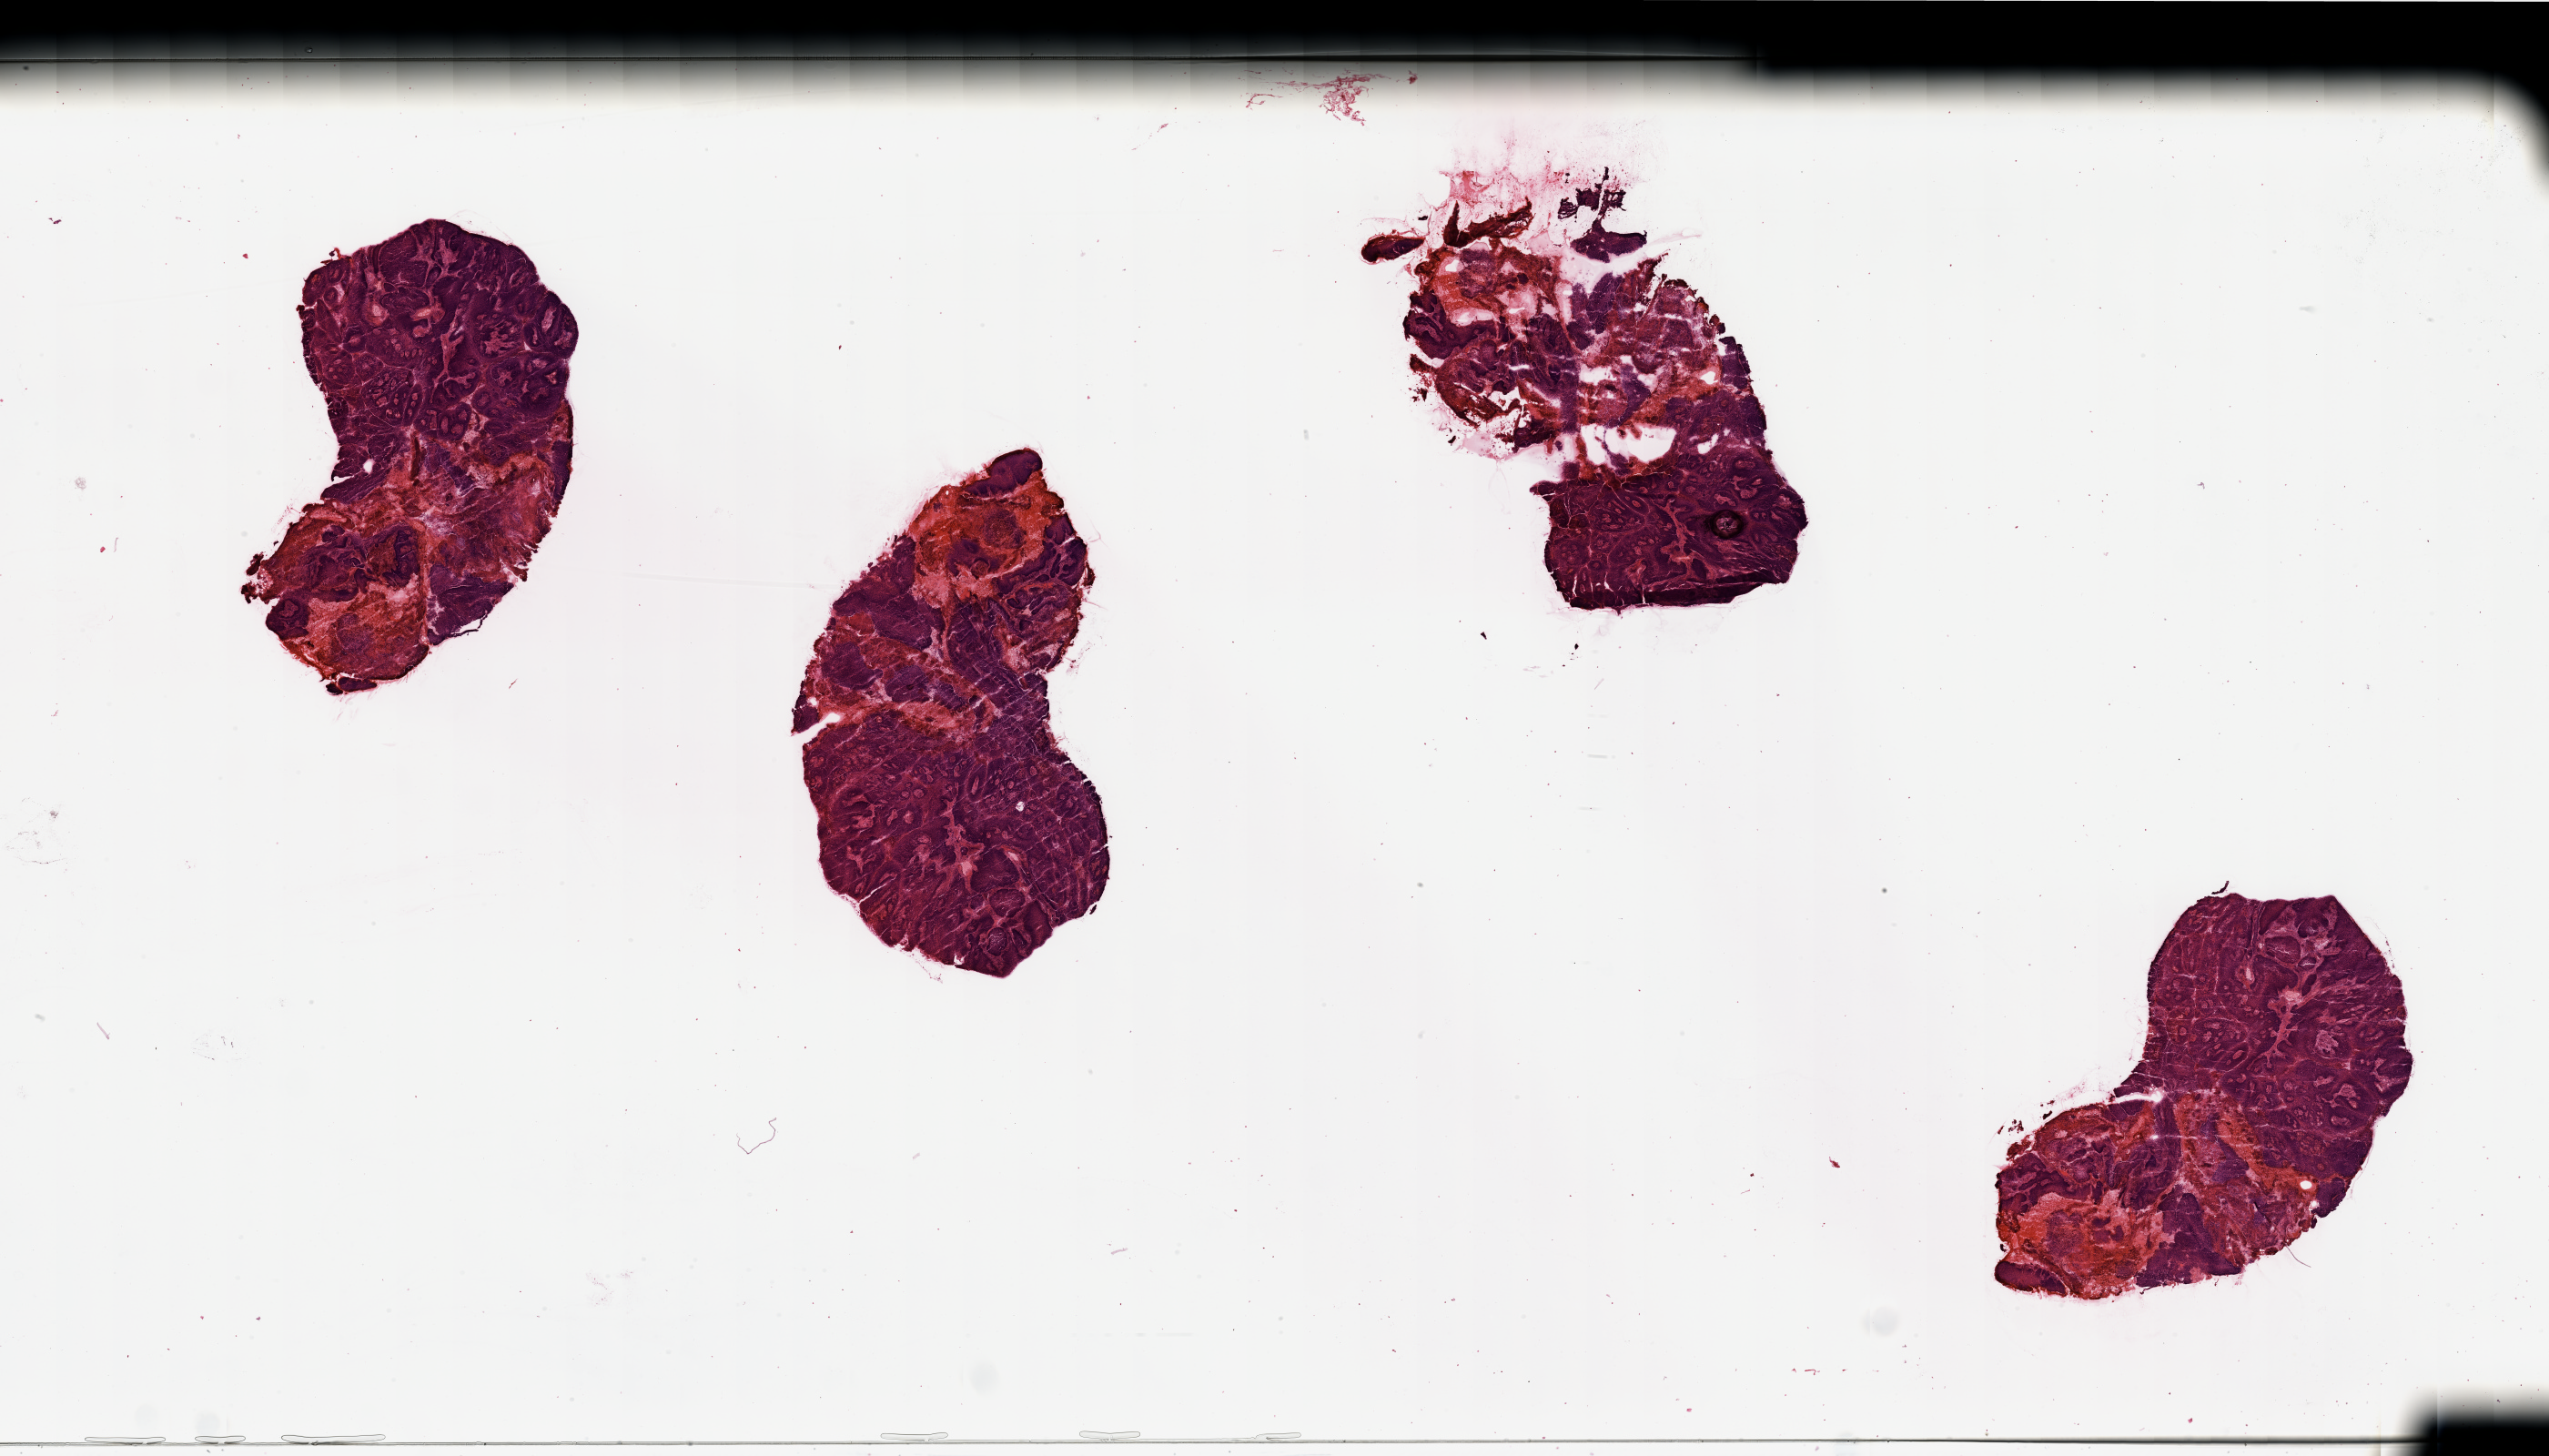
Whole-slide histology image, H&E — a low-resolution overview of the entire scanned area, about 44.3 x 25.3 mm. Head and neck, tissue type not recorded. Patient: male, age 63 years.
* patient diagnosis: Squamous cell carcinoma, NOS